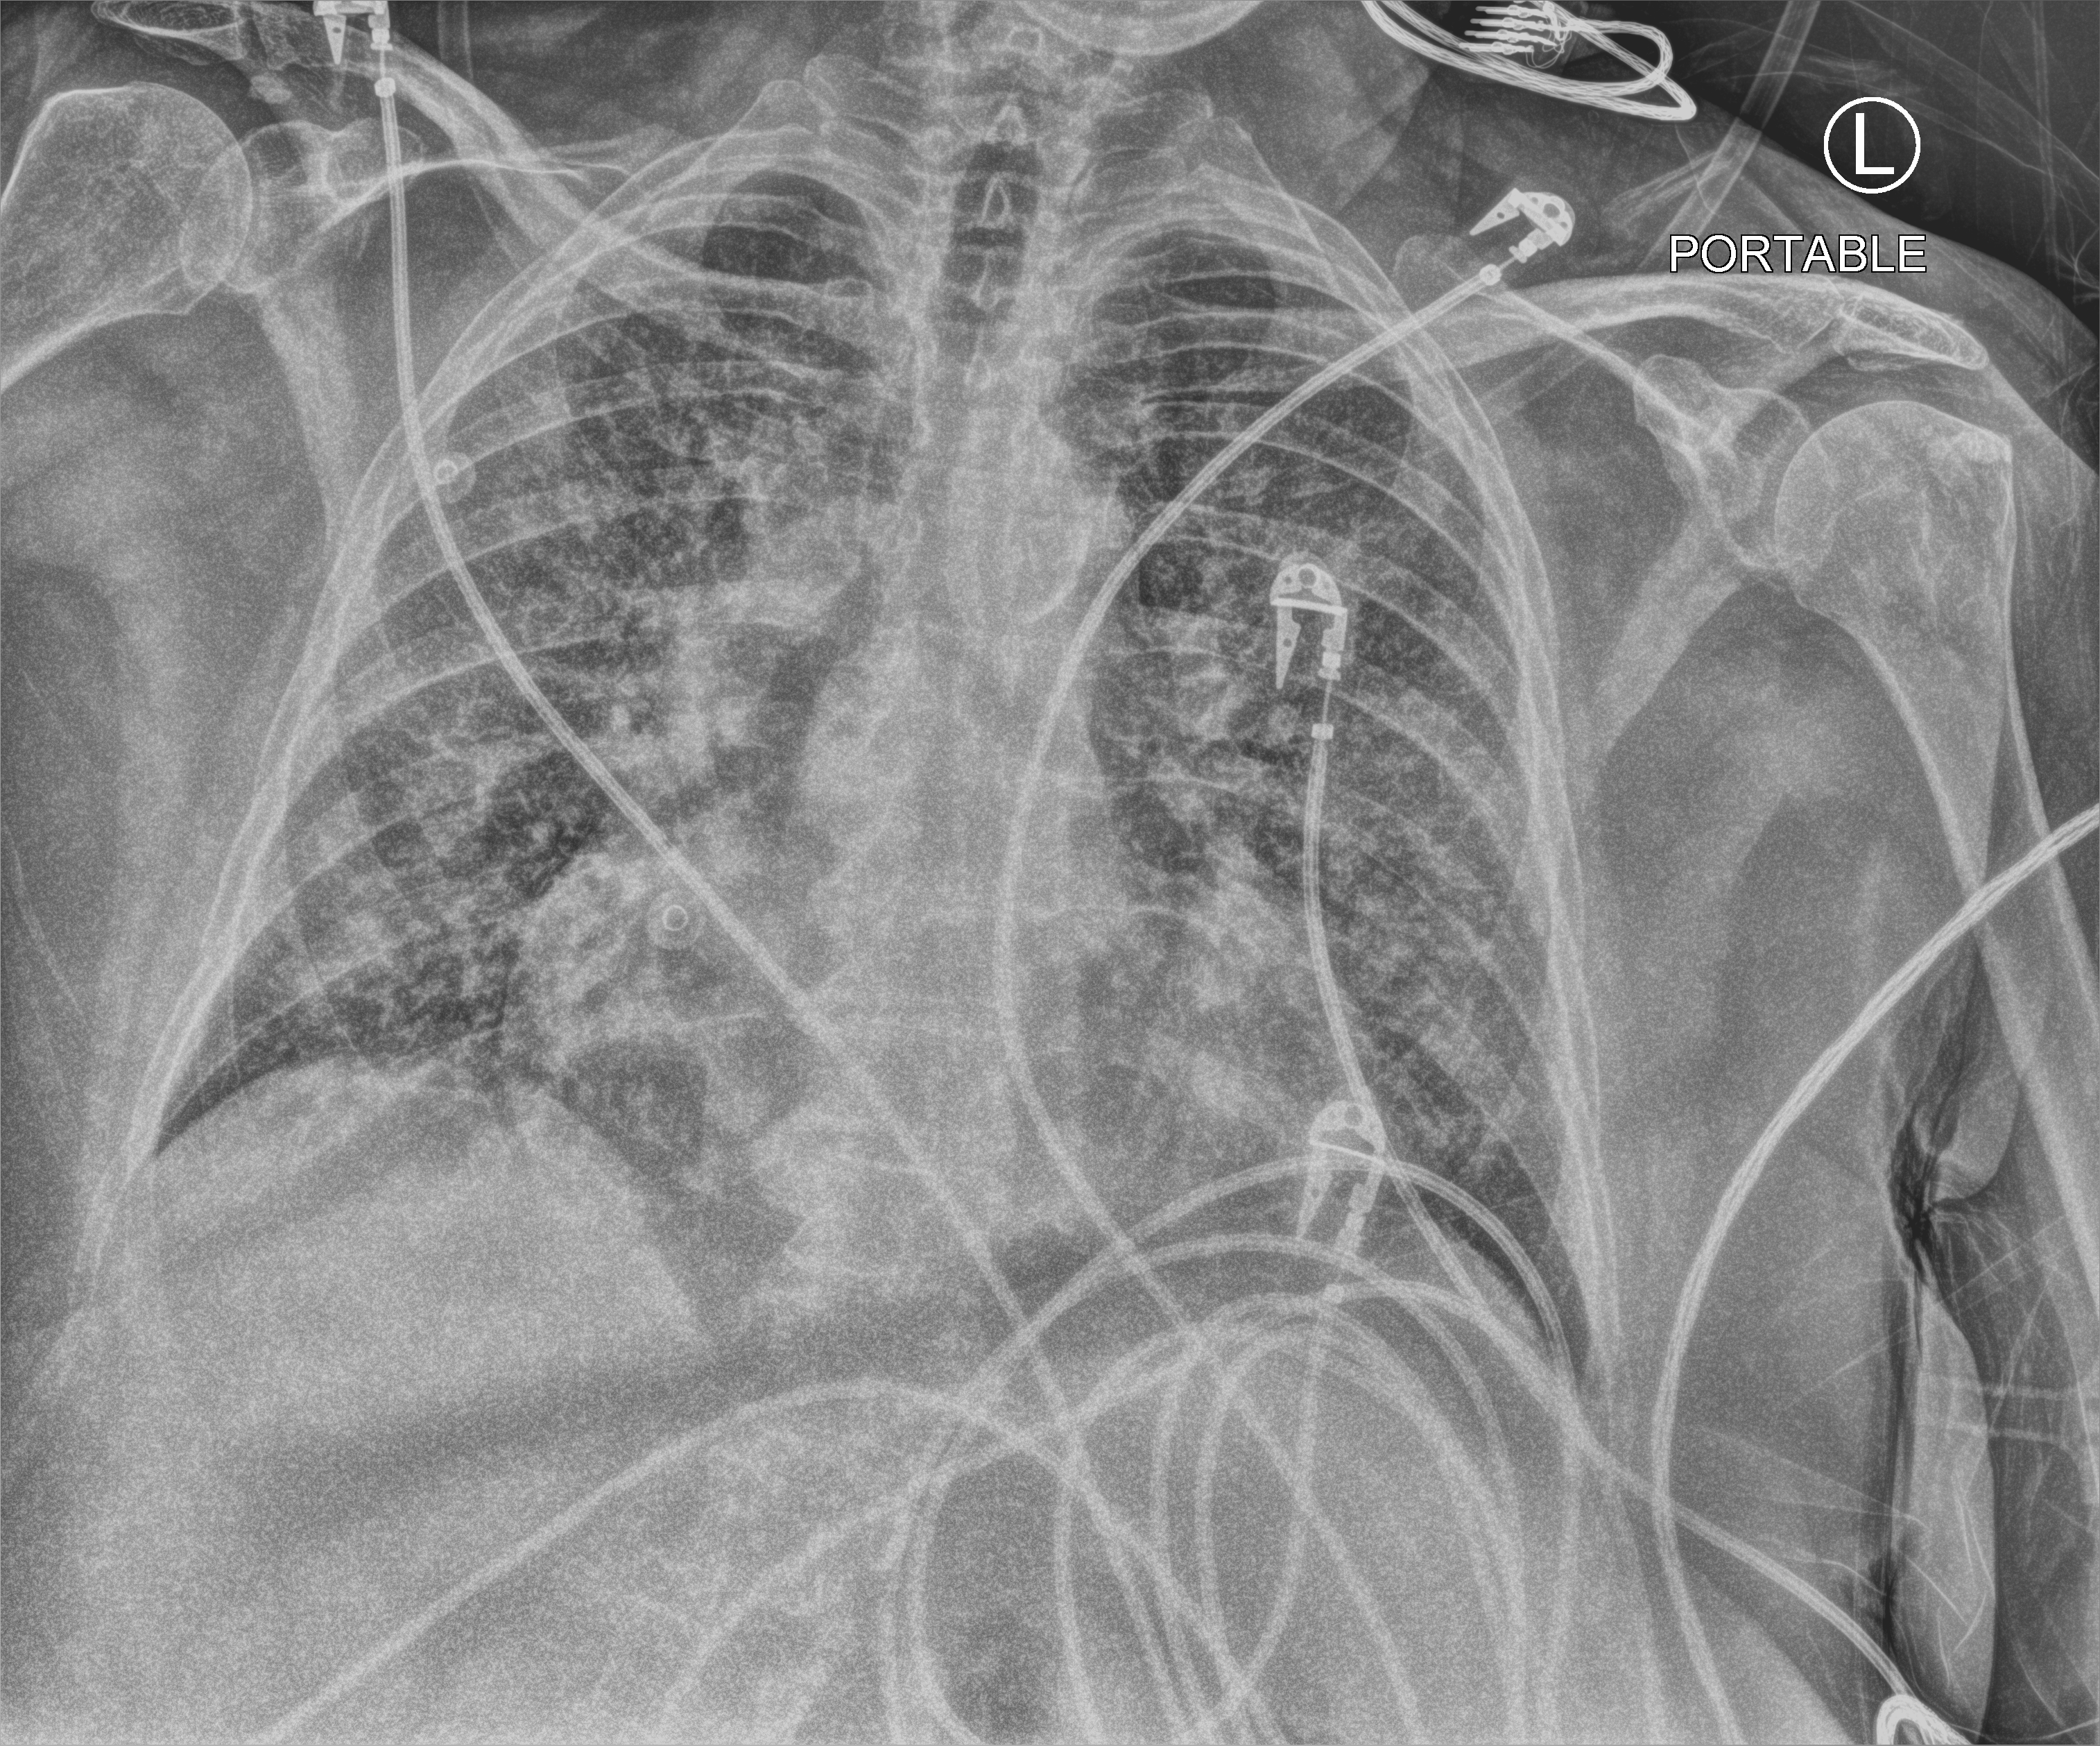
Portable chest radiograph; anteroposterior (AP) projection. Female patient hospitalised with COVID-19, age 75–90 years.
From the hospital-stay record, not from the radiograph (when in the stay this image was taken is not recorded):
- admitted to intensive care during this hospital stay: yes